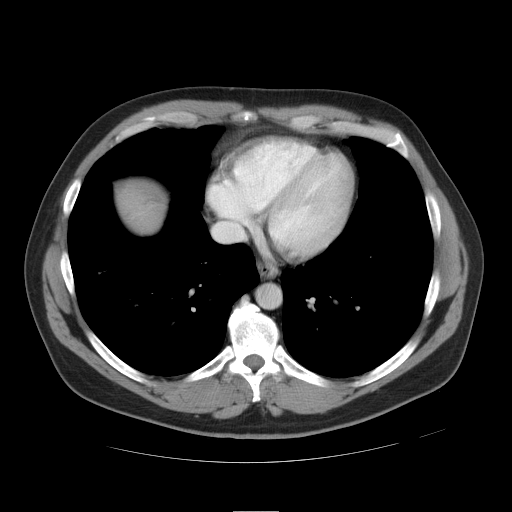
Contrast-enhanced abdominal CT, one axial slice. Slice 45 of 49 in the series (ordered by position). Reconstruction kernel STANDARD. 120 kVp. Intravenous contrast given. Soft-tissue window (W 400 / L 40 HU). 5 mm slice thickness. 512 × 512 image matrix, field of view 425 × 425 mm. Male patient, age 52 years. Case-level facts recorded for this patient, not image findings: diagnosis: colorectal cancer liver metastases, imaged before liver resection; multiple liver metastases: yes; largest metastasis: 5.1 cm.
Annotated regions visible in this slice (manually delineated by an expert):
- liver: box from (x=126, y=196) to (x=159, y=227) px